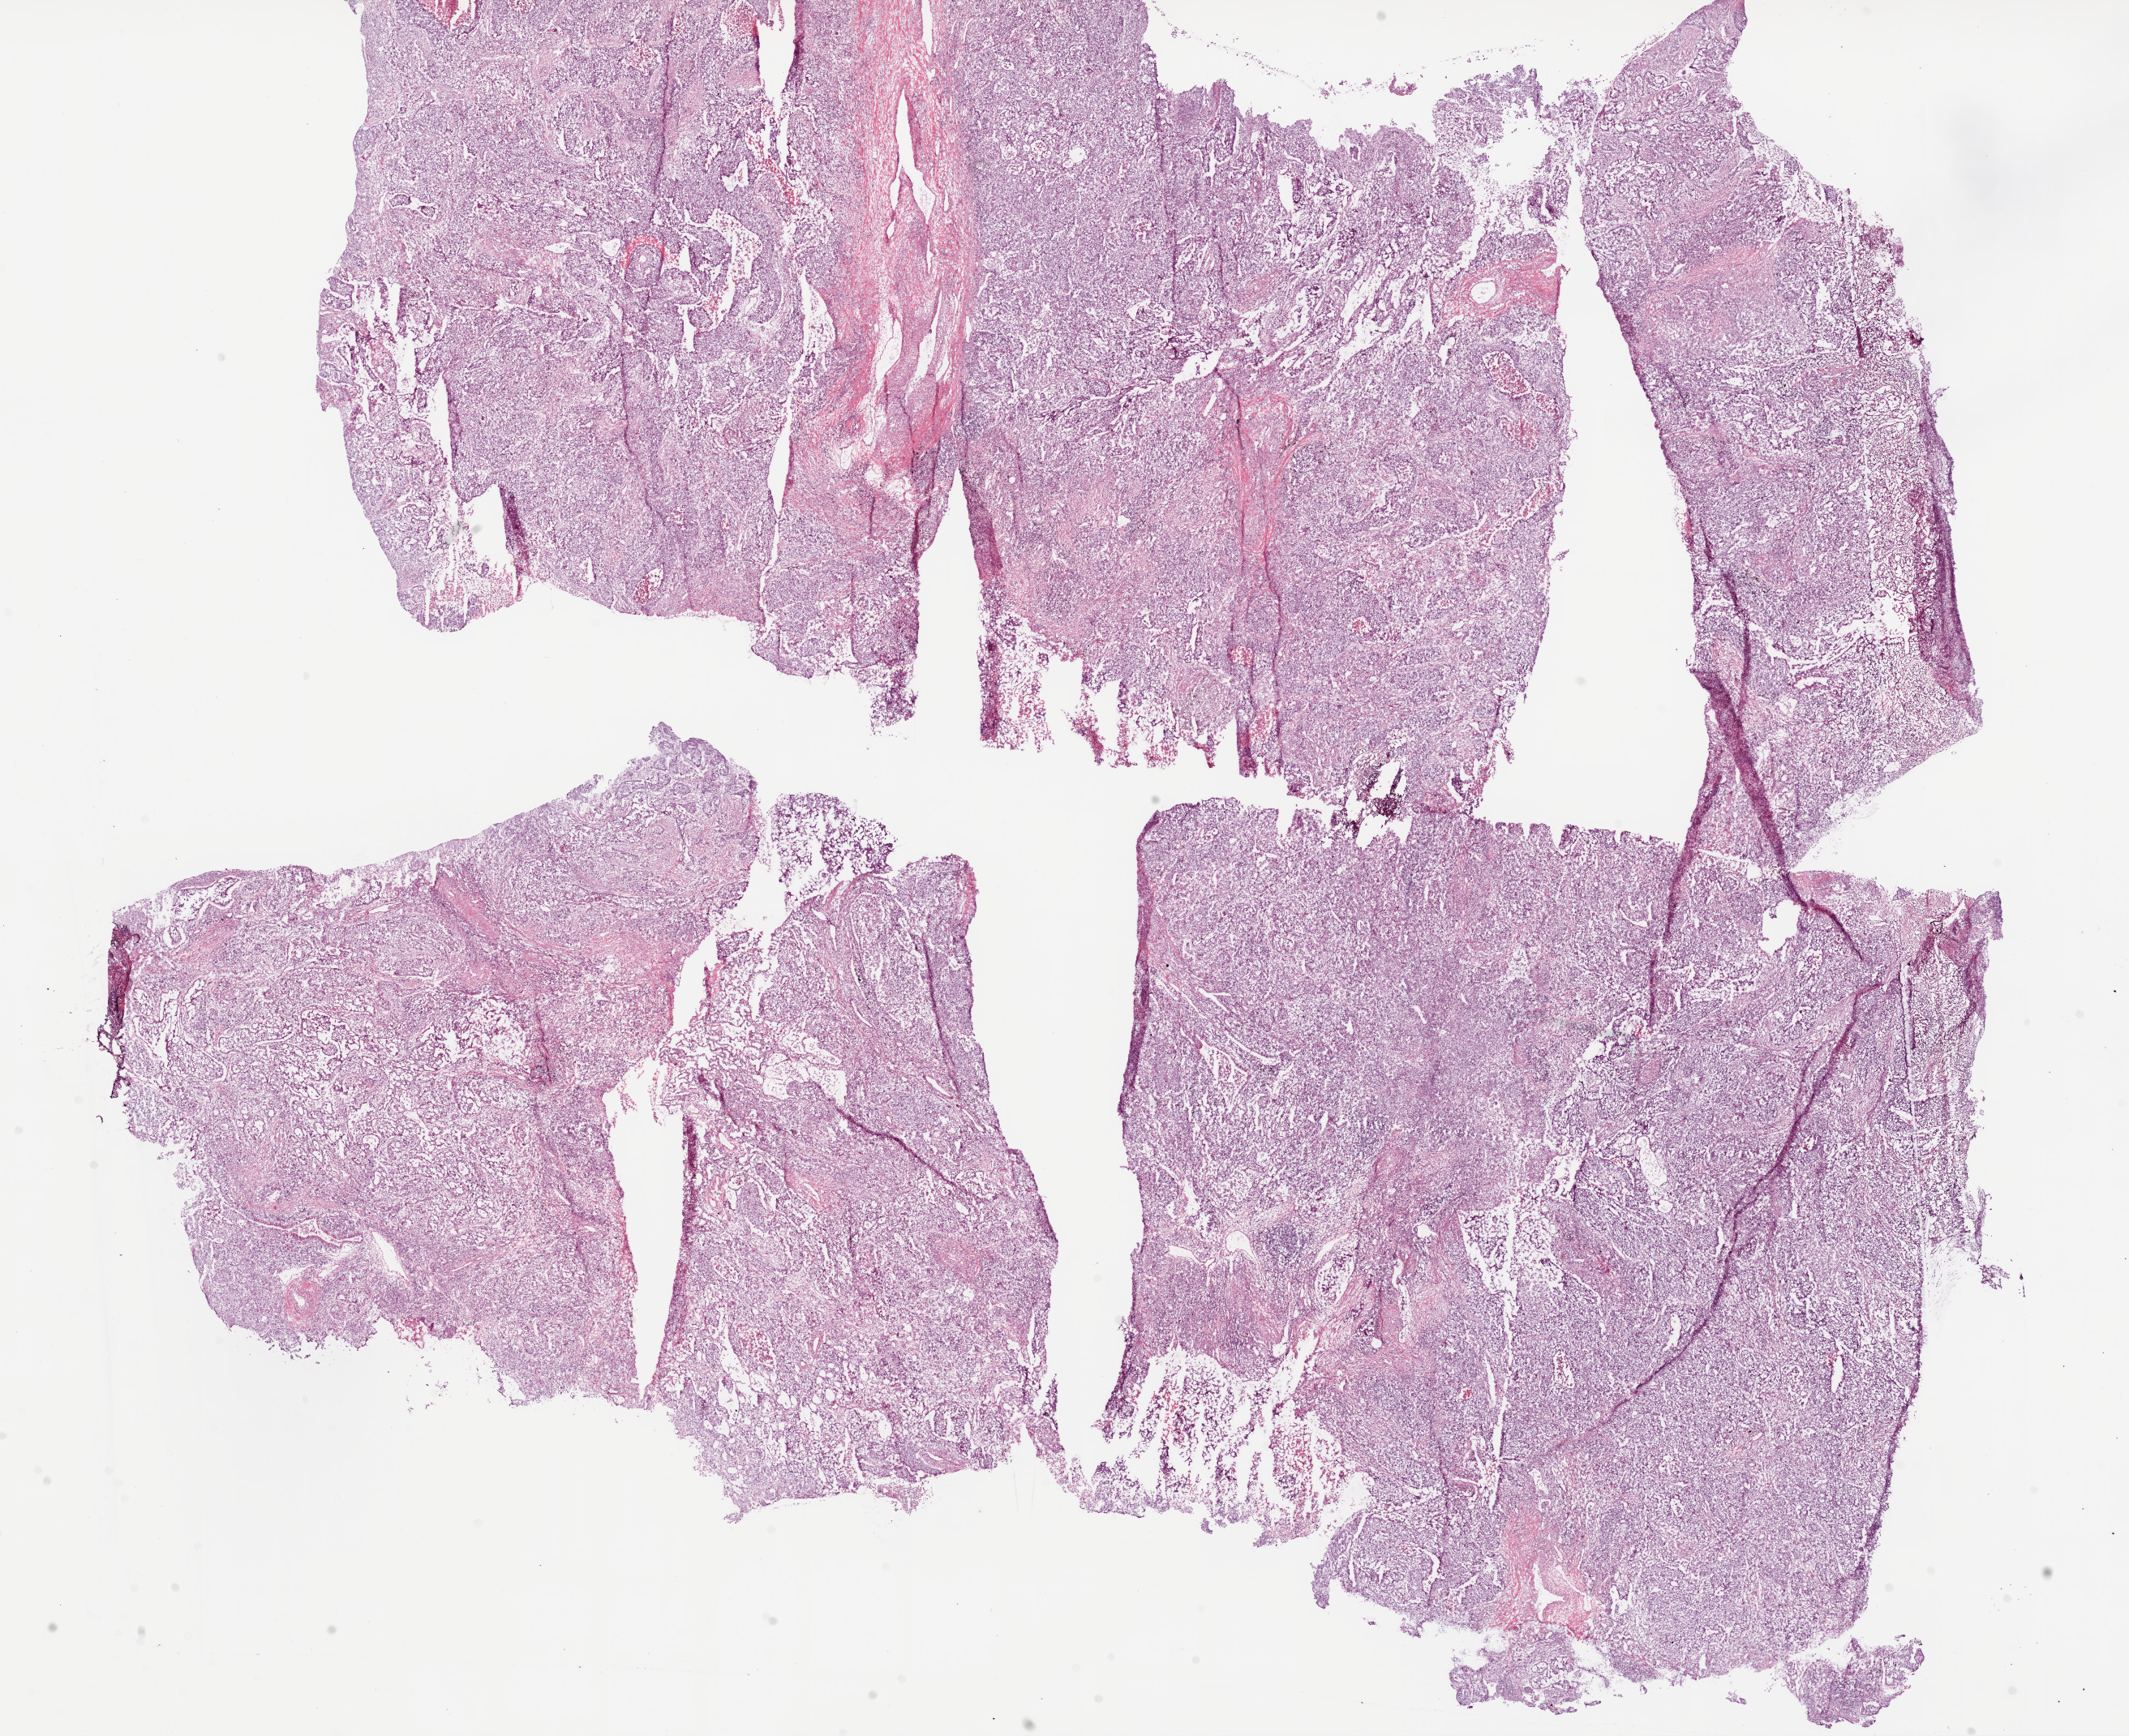
Whole-slide histology image, Hematoxylin and eosin (H&E) stained — shown as a low-resolution overview of the whole scanned area (about 21.1 x 17.2 mm, acquisition: 20x scan); frozen section from the top of the tissue portion; sample: primary tumour, lung. Male, age 70 years at initial diagnosis. Composition of this section per pathologist review: tumour cells 92%, tumour nuclei 70%, normal cells 0%, stromal cells 5%, necrosis 3%. Inflammatory infiltration, as recorded: lymphocyte infiltration 20%, monocyte infiltration 2%, neutrophil infiltration 5%.
Pathologic diagnosis: Squamous cell carcinoma, NOS. AJCC pathologic stage: IB.